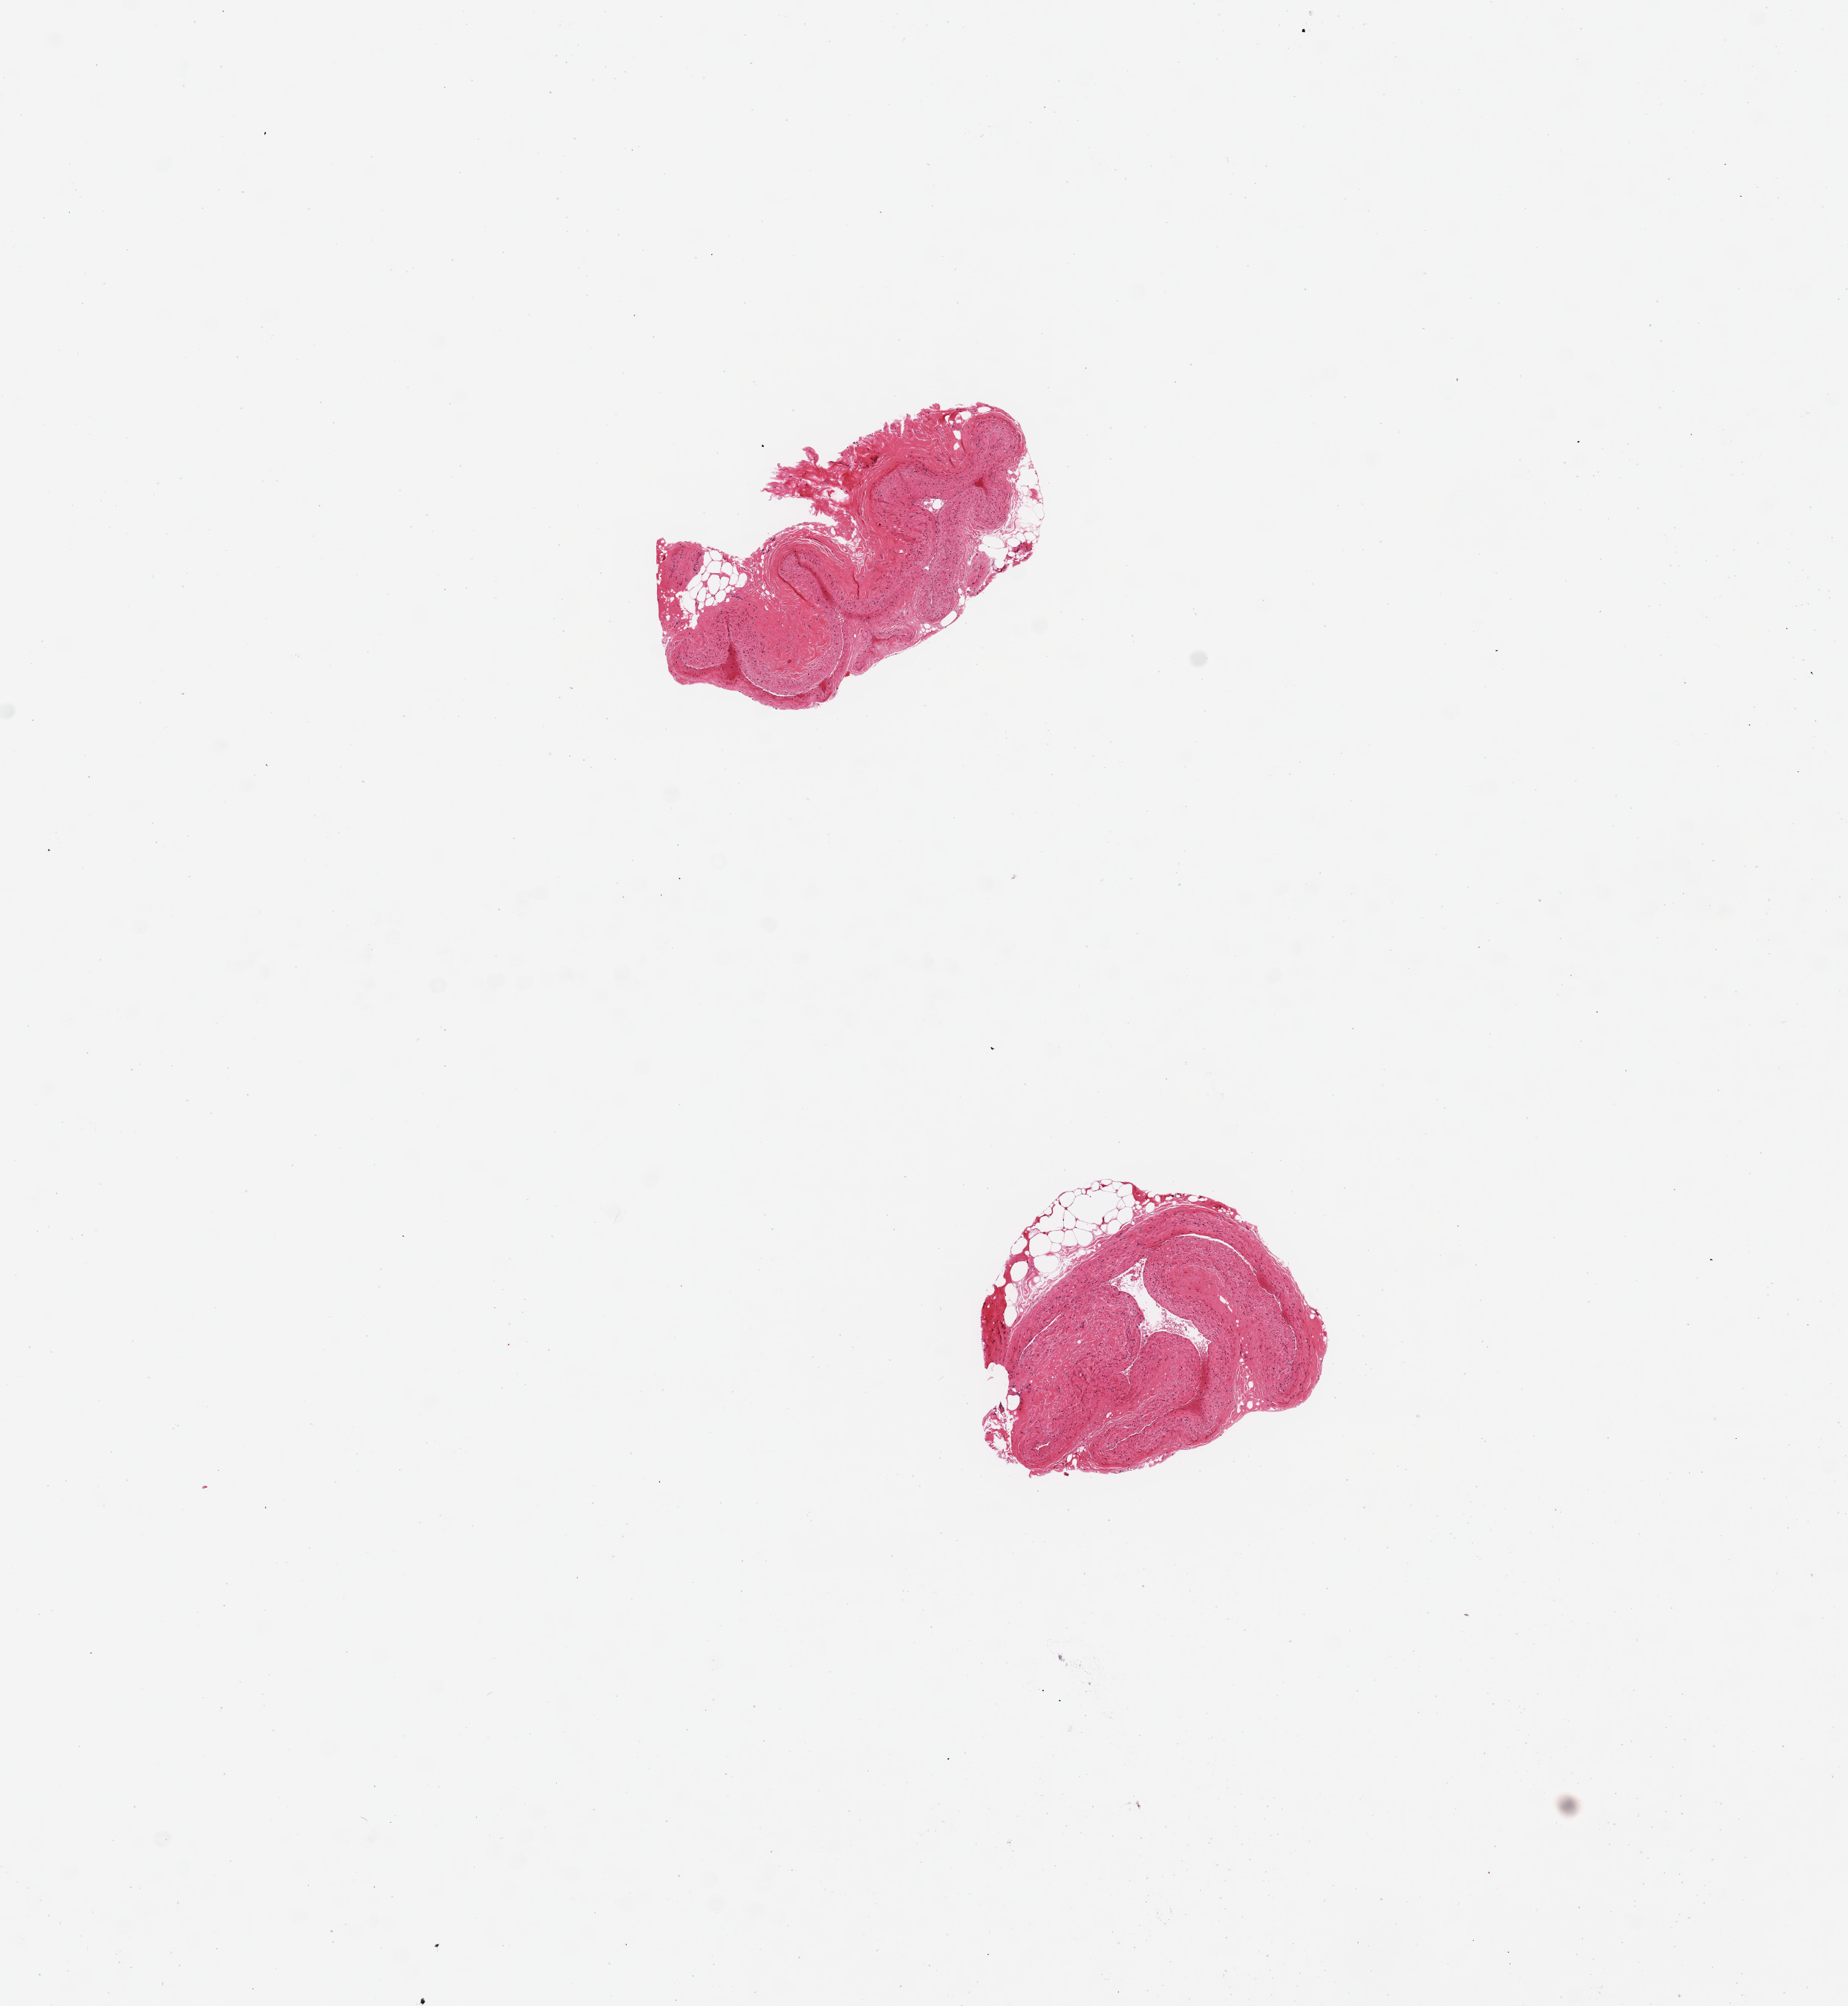
Digitized haematoxylin and eosin-stained section, brightfield, a low-resolution overview of the entire scanned area, about 9.8 x 10.7 mm; PAXgene-fixed, paraffin-embedded tissue; section of coronary artery (target tissue); tissue donor sample. Donor: male.
- reviewer comment on this tissue sample: 2 pieces, probably marginal branch, not main coronary artery